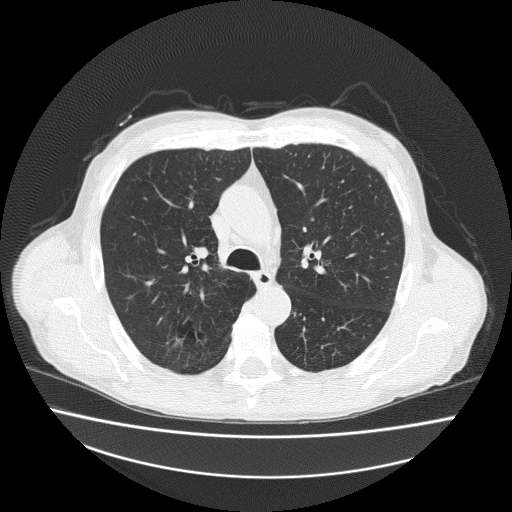
Axial slice from a low-dose chest CT screening exam, second screening round (one year after baseline), lung window (W 1500 / L -600 HU), 120 kVp, slice 69 of 186 in the series. Male participant, aged 73 years at enrolment. Current smoker at enrolment.
• Expert reader's lesion annotation, box from (x=160, y=315) to (x=215, y=360) px.
• Screening reader's record for this exam: no non-calcified nodule ≥4 mm recorded.
• Later outcome: lung cancer diagnosed 418 days after this screen — adenosquamous carcinoma, right upper lobe, well differentiated (G1), stage IA (AJCC 6th edition), 20 mm at pathology.